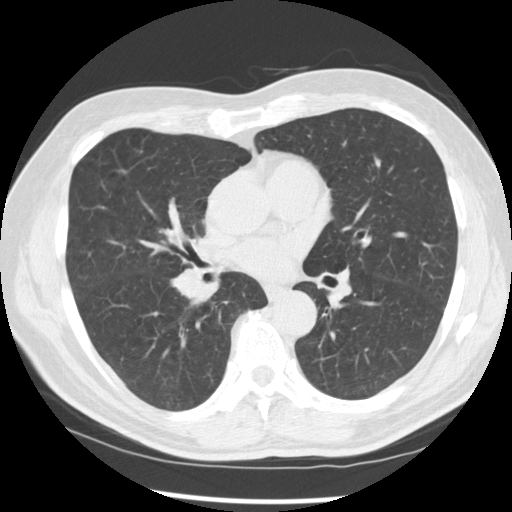
Axial slice from a low-dose chest CT screening exam; first (baseline) screen; lung window (W 1500 / L -600 HU); 2.5 mm slice thickness; standard (soft-tissue) reconstruction kernel (STANDARD); slice 145 of 277 in the series. Male participant, aged 67 years at enrolment. Current smoker at enrolment.
Expert-annotated lung lesion, bounding box (x1, y1, x2, y2) in pixels: (157, 246, 228, 312). Reader record for this screening exam (exam-level; its link to the box is not recorded): non-calcified nodule or mass ≥4 mm, left lower lobe, 15 × 15 mm, spiculated (stellate) margins, soft tissue attenuation. Note: the box lies in the patient's right hemithorax on this image, whereas the reader's record names the left lung; they may be different findings. Official screen result: positive, change unspecified: nodule(s) >= 4 mm or enlarging nodule(s), mass(es), or other non-specific abnormalities suspicious for lung cancer.